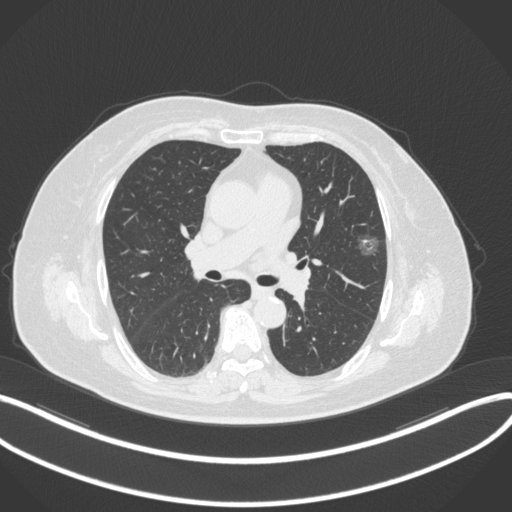
Chest CT, one axial slice. Slice 180 of 286 in the series (ordered by position). Reconstruction kernel B31f. Lung window (W 1500 / L -600 HU). 512 × 512 image matrix. Female patient, age 76 years. From the clinical record (not read from this slice): clinical TNM (as recorded): T1b N0 M0; histopathological grade: G1-2.
Outlined on this slice (rectangle marked by the reading radiologist):
- lung tumour (recorded histology: adenocarcinoma): box from (x=354, y=228) to (x=384, y=259) px